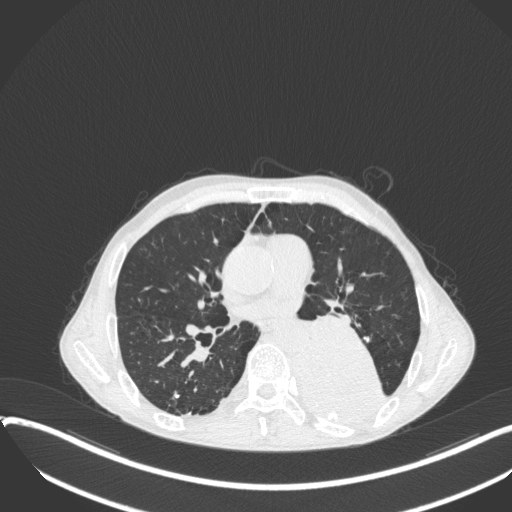
Chest CT, one axial slice. Position 191 of 400 along the scan axis. 120 kVp. Lung window (W 1500 / L -600 HU). 1 mm slice thickness. 512 × 512 image matrix, field of view 400 × 400 mm. Male patient, age 57 years. Case-level facts recorded for this patient, not image findings: clinical TNM (as recorded): T4 N0 M0.
Annotated regions visible in this slice (rectangle marked by the reading radiologist):
- lung tumour (recorded histology: squamous cell carcinoma): bounding box [x1, y1, x2, y2] px = [283, 325, 389, 426]